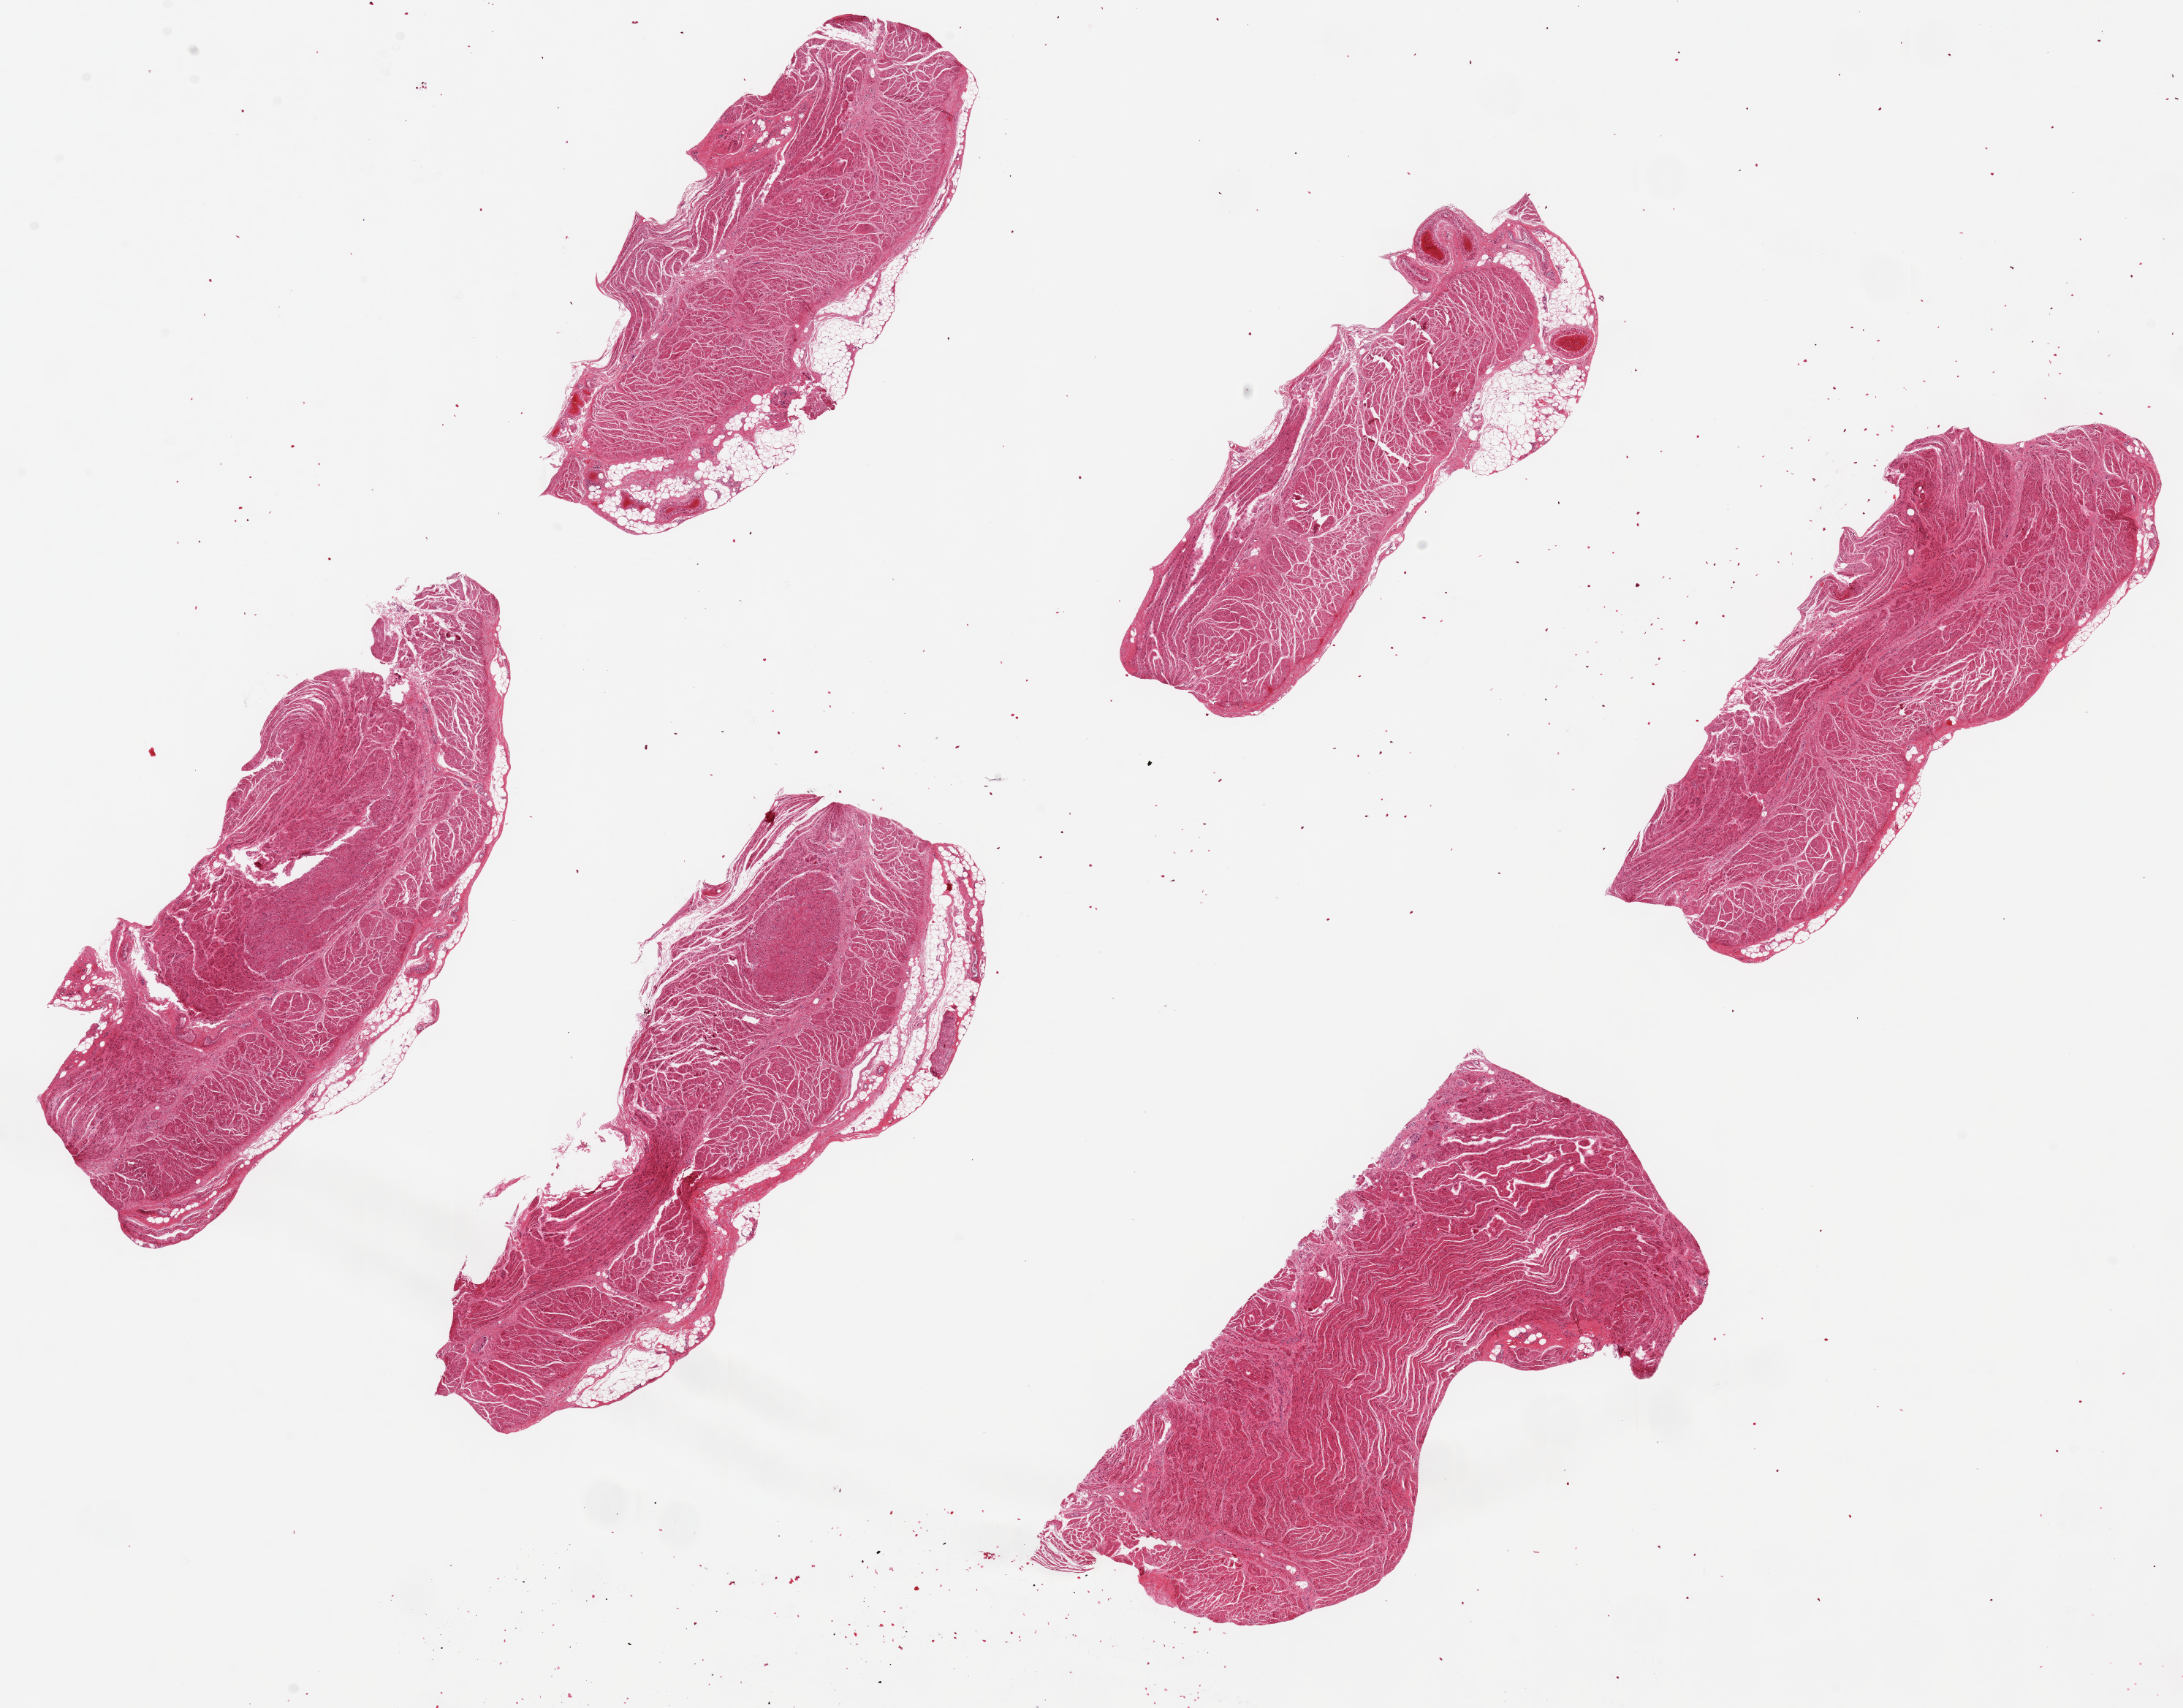
Digitized hematoxylin and eosin (H&E)-stained section, shown as a low-resolution overview of the whole scanned area (about 23.6 x 18.5 mm). PAXgene-fixed, paraffin-embedded tissue. Section of gastroesophageal junction (target tissue). Tissue donor sample. Male donor.
Review note (as recorded): 6 pieces, up to 8x3.5mm; all muscle, no mucosa; 20% adipose on deep surface in 3 of 6 pieces.